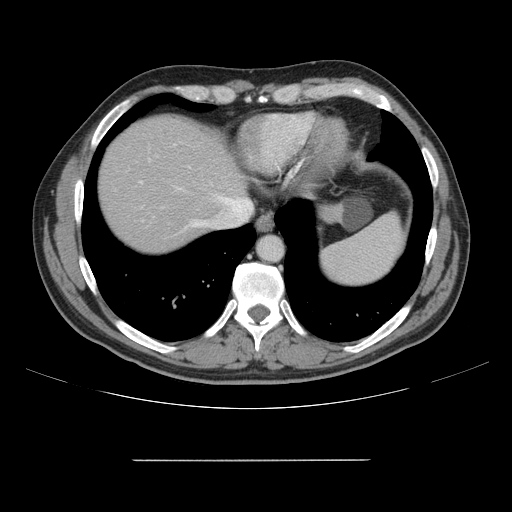
Contrast-enhanced abdominal CT, one axial slice; slice 136 of 164 in the series (ordered by position); 120 kVp; intravenous contrast given; soft-tissue window (W 400 / L 40 HU); 2.5 mm slice thickness; 512 × 512 image matrix, field of view 404 × 404 mm. Male patient, age 54 years. From the clinical record (not read from this slice): diagnosis: colorectal cancer liver metastases, imaged before liver resection; multiple liver metastases: yes; largest metastasis: 1 cm; disease in both lobes: no.
Structures marked on this image (manually delineated by an expert):
- hepatic veins: bounding box [x1, y1, x2, y2] px = [175, 187, 253, 231]
- liver: [99, 118, 244, 253]
- planned liver remnant (the part of the liver to remain after resection): [99, 118, 244, 253]
- portal vein (with intrahepatic branches): [140, 160, 150, 183]